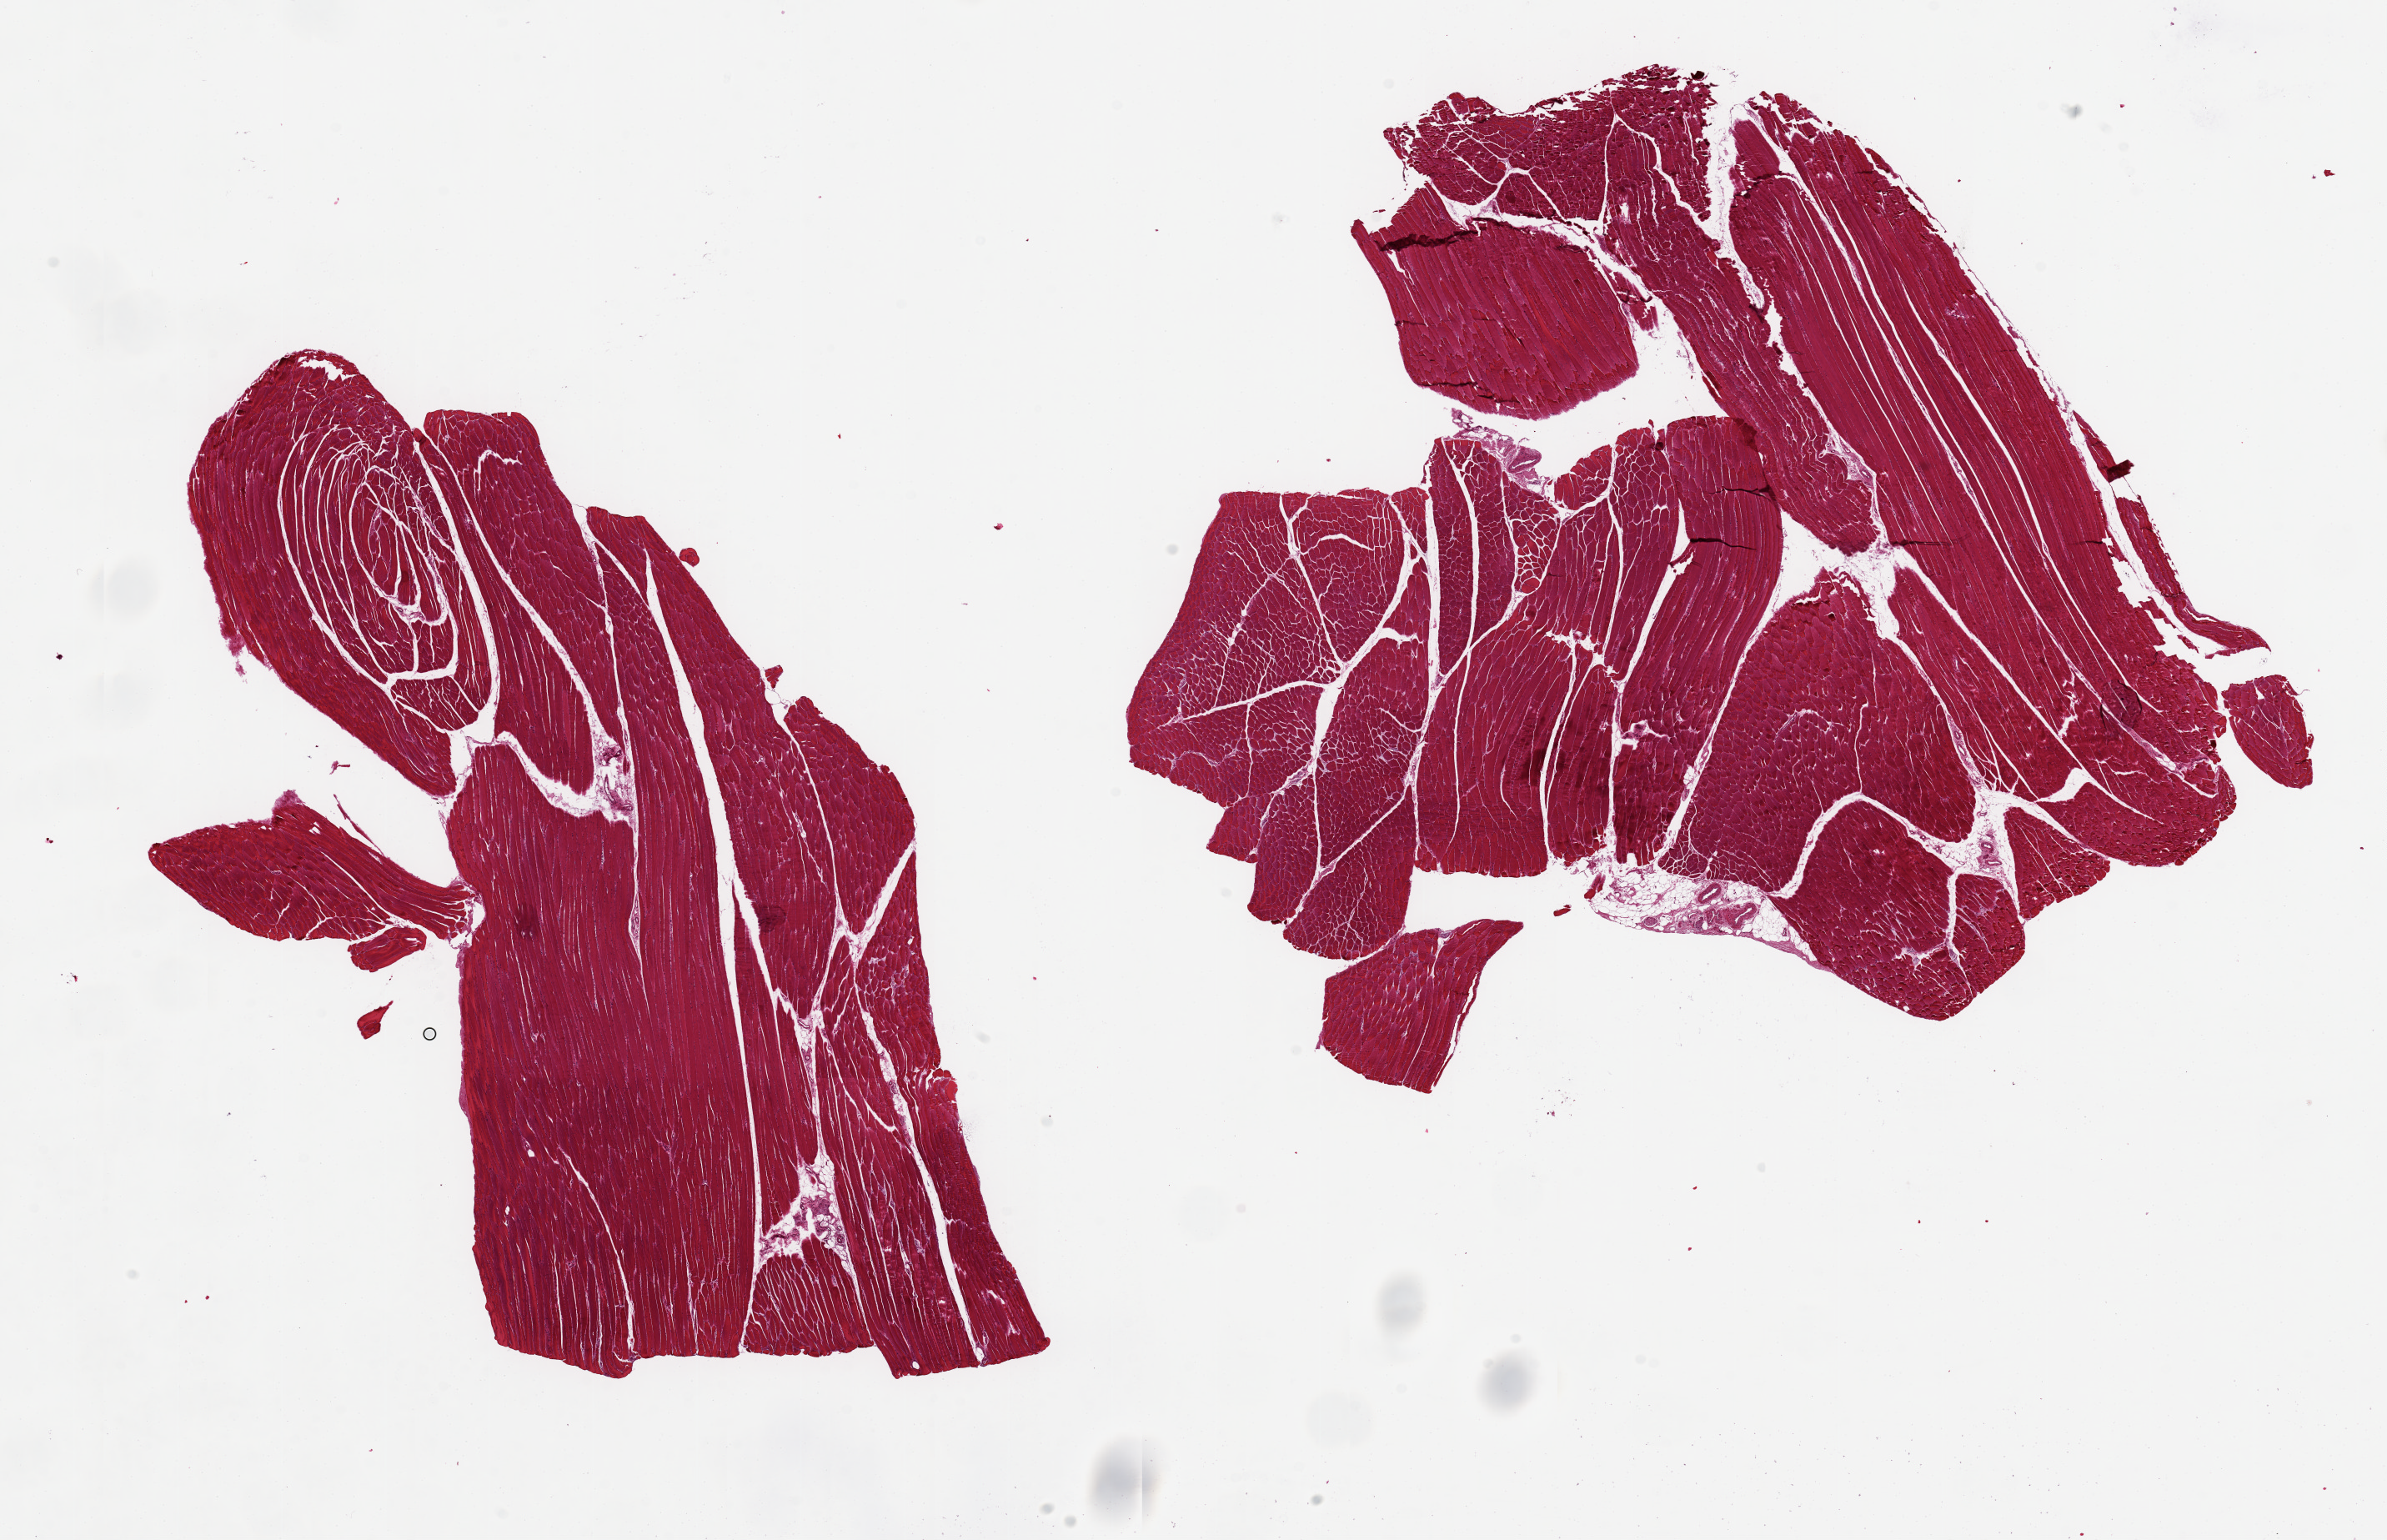
Haematoxylin and eosin whole-slide image — a low-resolution overview of the entire scanned area, about 22.6 x 14.6 mm (acquisition: 20x scan). PAXgene-fixed paraffin-embedded (PFPE) section. Target tissue: skeletal muscle. Tissue donor sample.
Pathologist's review note for this sample: 2 pieces 9x9 & 9x5 mm; clean except for a 1 mm nodule of fibroadipose.